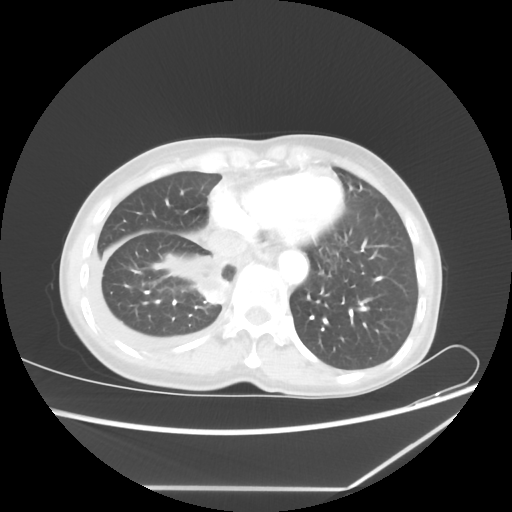
Chest CT, one axial slice; 80 kVp; lung window (W 1500 / L -600 HU); 5 mm slice thickness; 512 × 512 image matrix, field of view 364 × 364 mm. Female patient, age 59 years. From the clinical record (not read from this slice): clinical TNM (as recorded): T1c N1 M1.
Structures marked on this image (rectangle marked by the reading radiologist):
- lung tumour (recorded histology: adenocarcinoma): bounding box <195,273,228,305> (left, top, right, bottom; pixels)